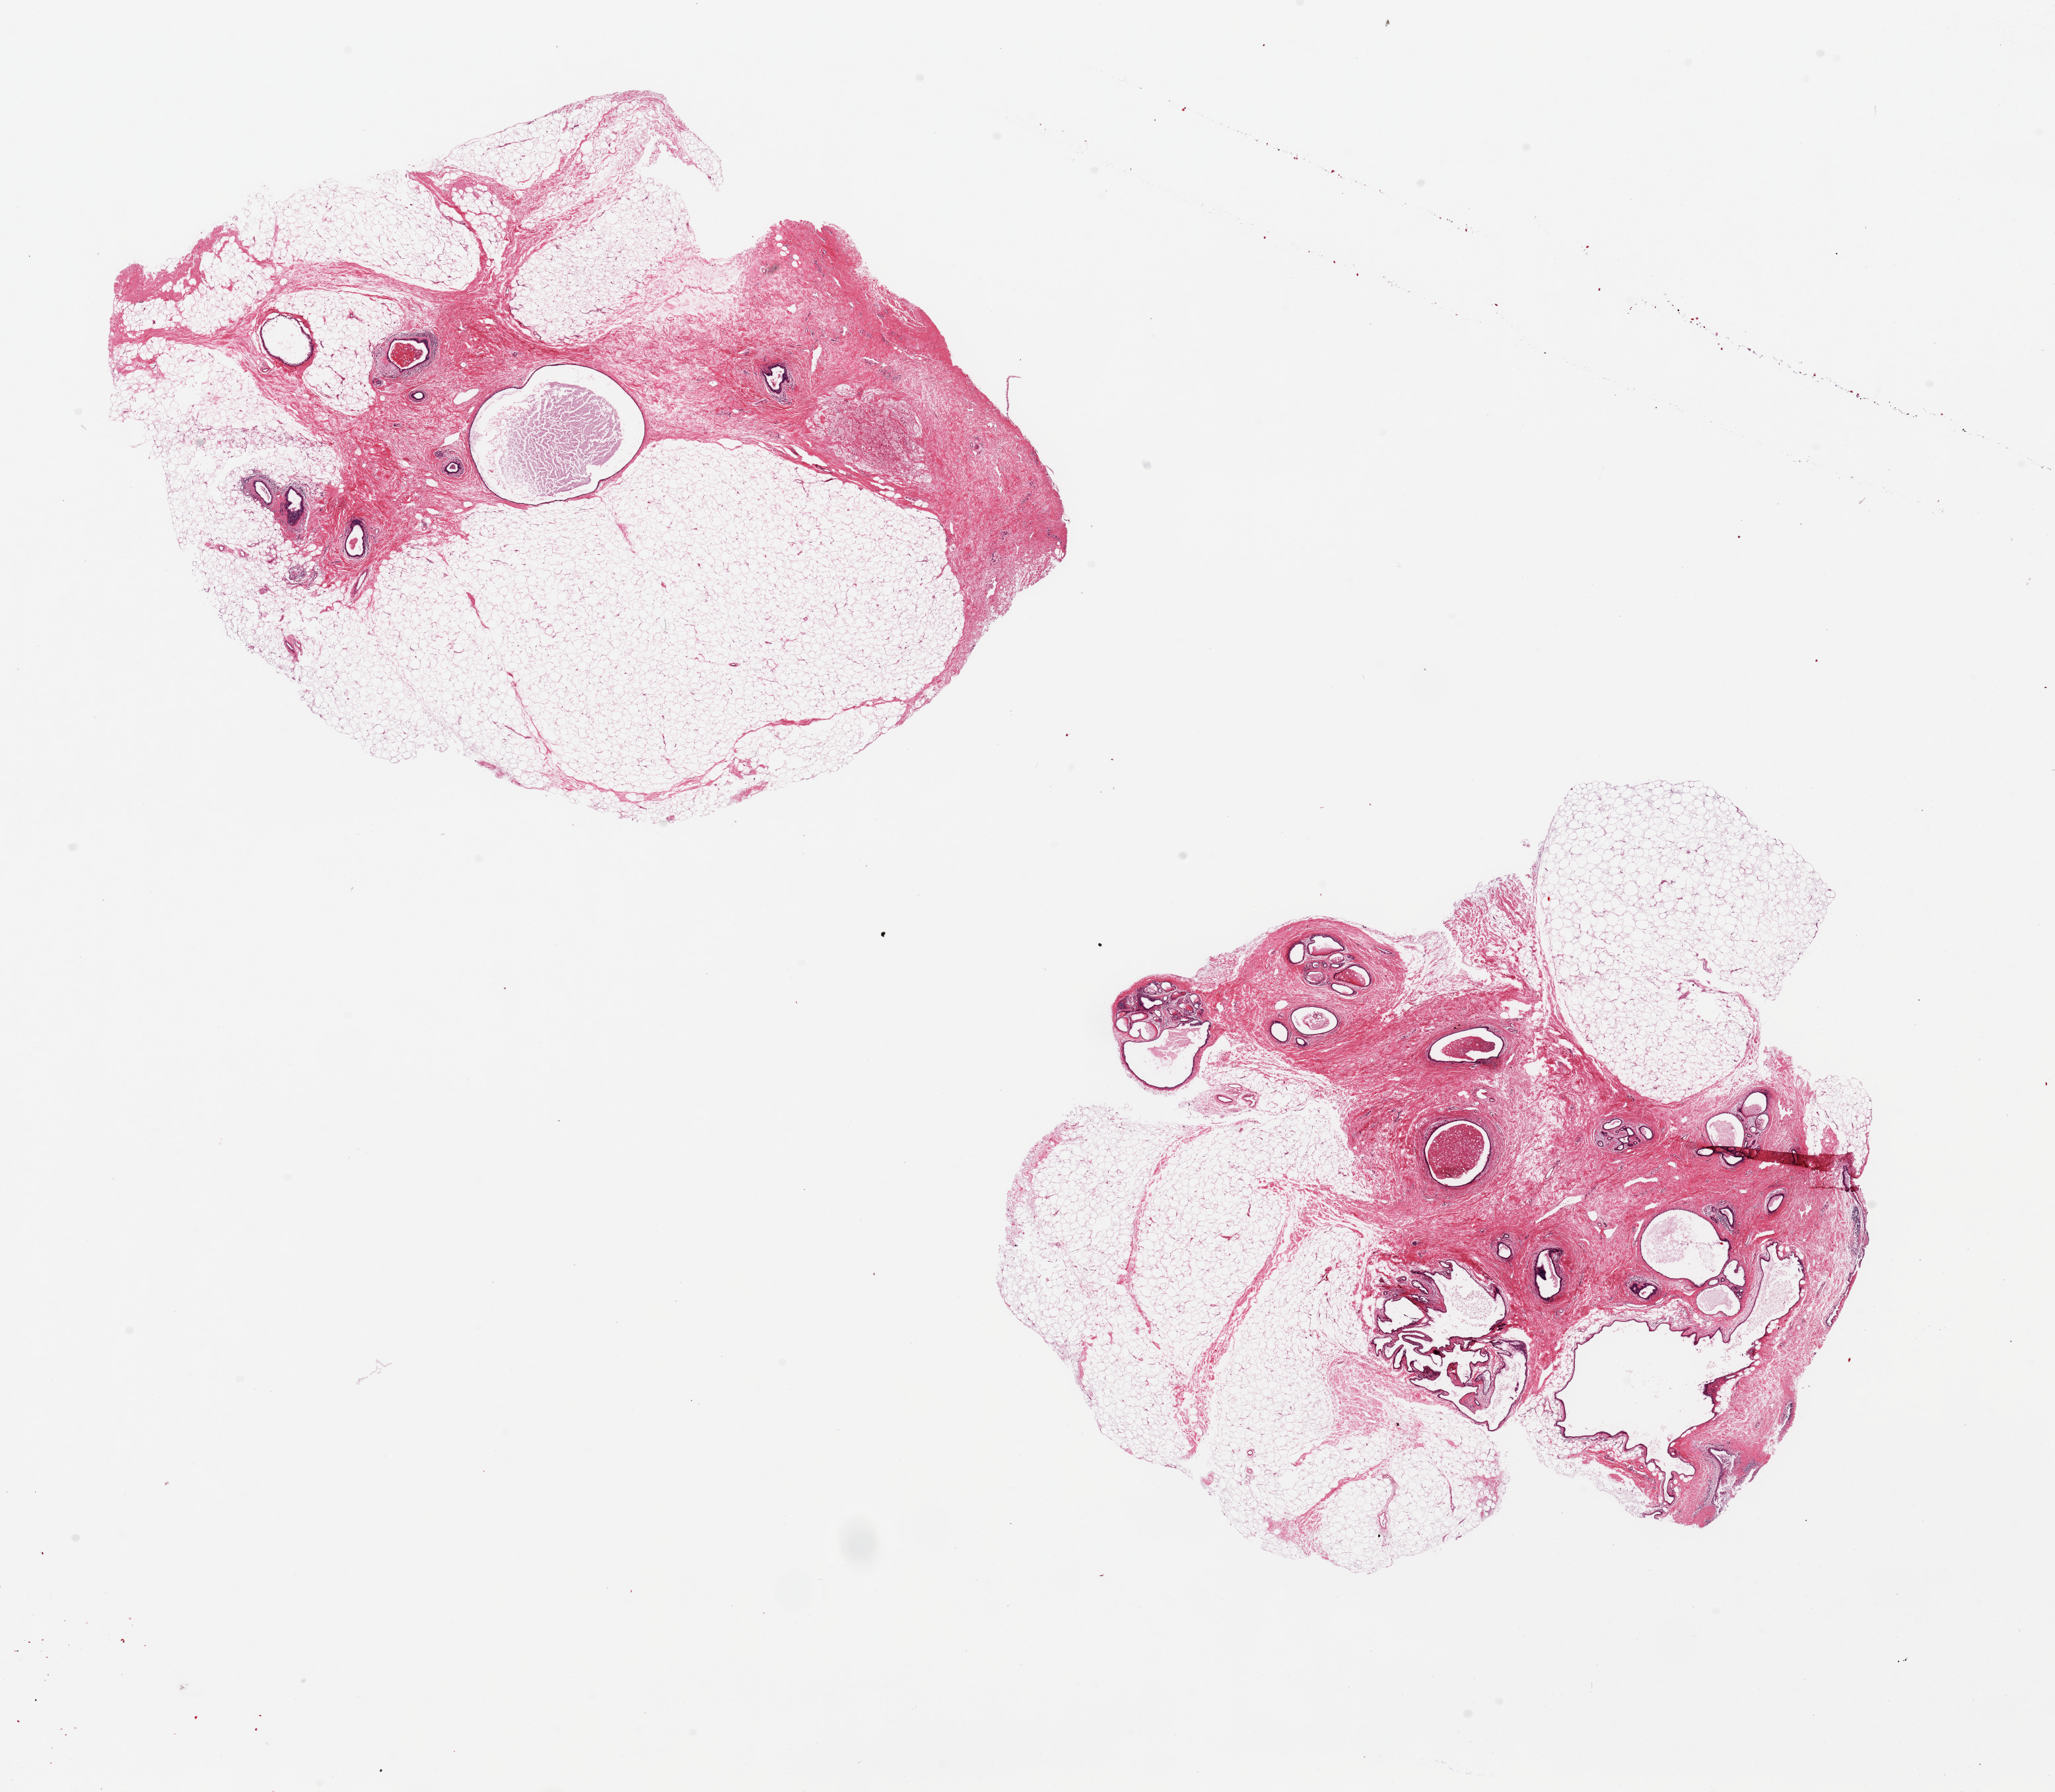
Digitized hematoxylin and eosin (H&E)-stained section — a low-resolution overview of the entire scanned area, about 24.6 x 21.5 mm; PAXgene-fixed, paraffin-embedded tissue; target tissue: breast; tissue donor sample. Donor: male.
Pathologist's review note for this sample: 2 pieces 10x7 & 11x7 mm; fibrocystic change in gynecomastia; 60% adipose.